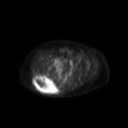
FDG PET of an extremity soft-tissue mass (from a PET/CT study), one axial slice; position 59 of 267 along the scan axis; 128 × 128 image matrix. Patient: female, 60 years. Case-level facts recorded for this patient, not image findings: histological type: spindle cell suggestive of myxofibrosarcoma; grade: intermediate; site of the primary tumour: right buttock.
Structures marked on this image (expert contour drawn on MRI and transferred to this co-registered scan by the dataset authors):
- gross tumour volume (mass): bounding box [x1, y1, x2, y2] px = [33, 76, 58, 95]